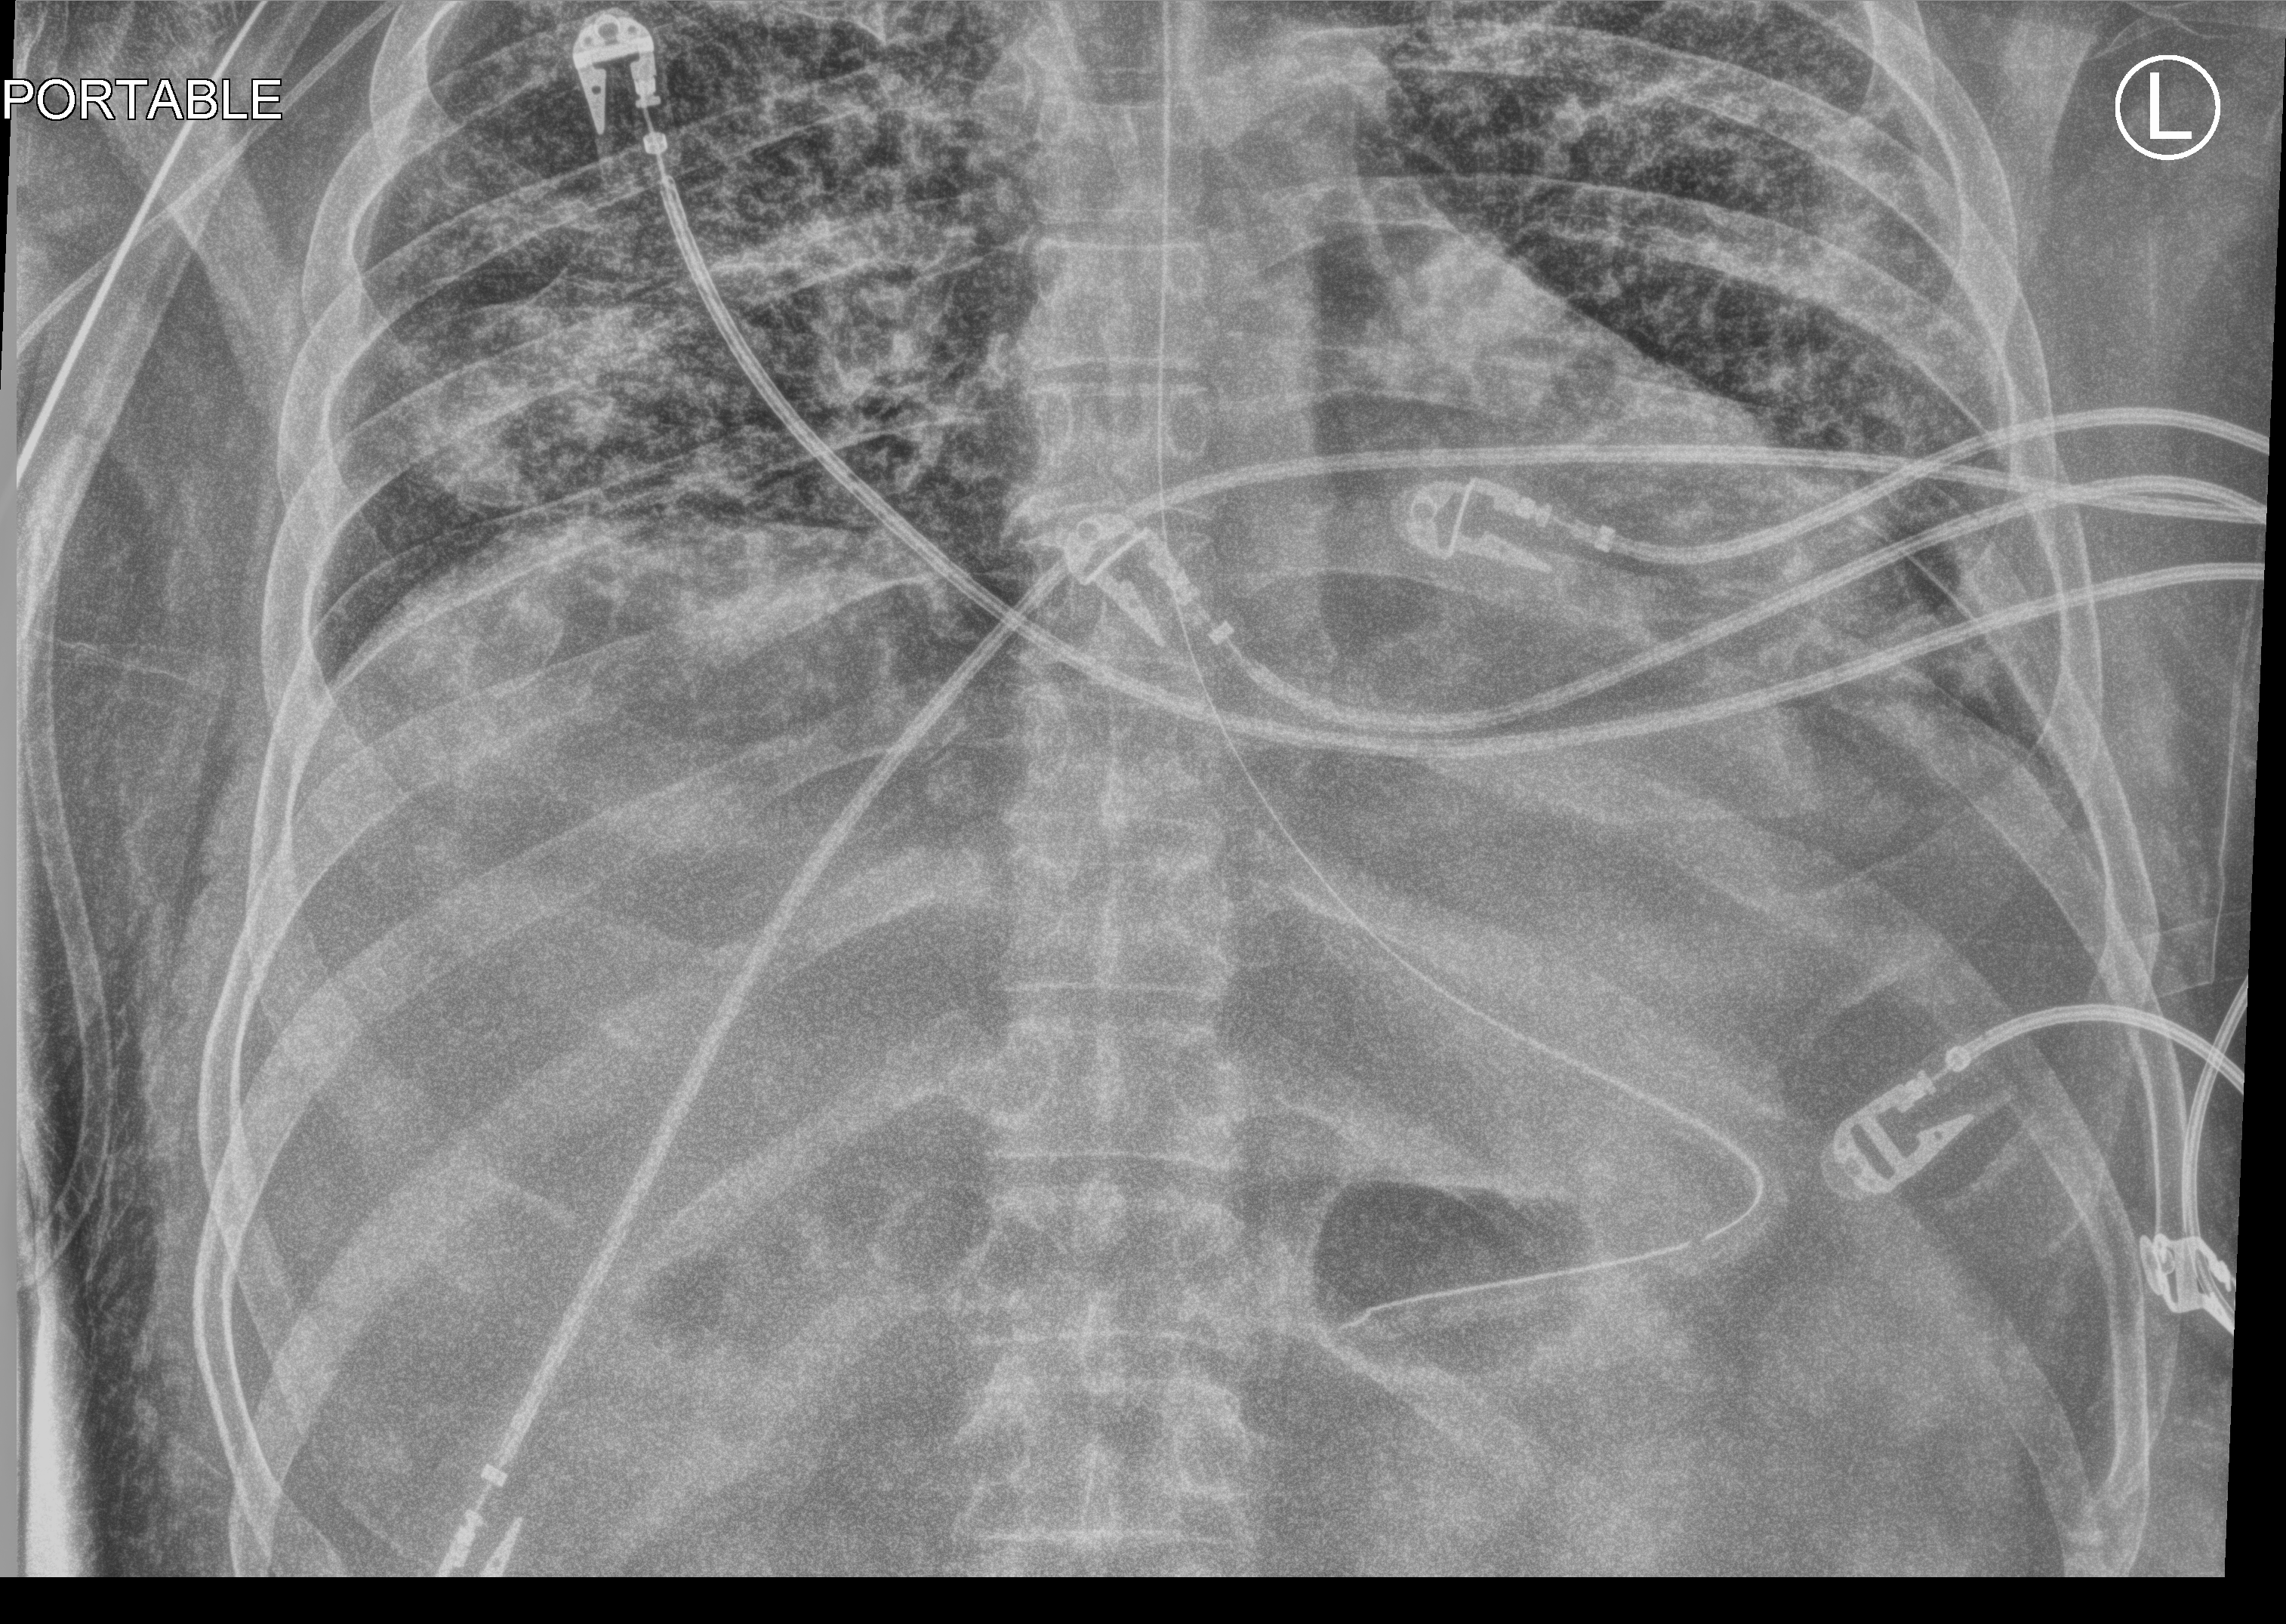
Chest X-ray (portable); anteroposterior (AP) projection. Patient hospitalised with COVID-19; male, aged 18–59 years.
Admission-level facts for this patient (not findings on this image; timing relative to this image not recorded): mechanically ventilated during this hospital stay: yes.